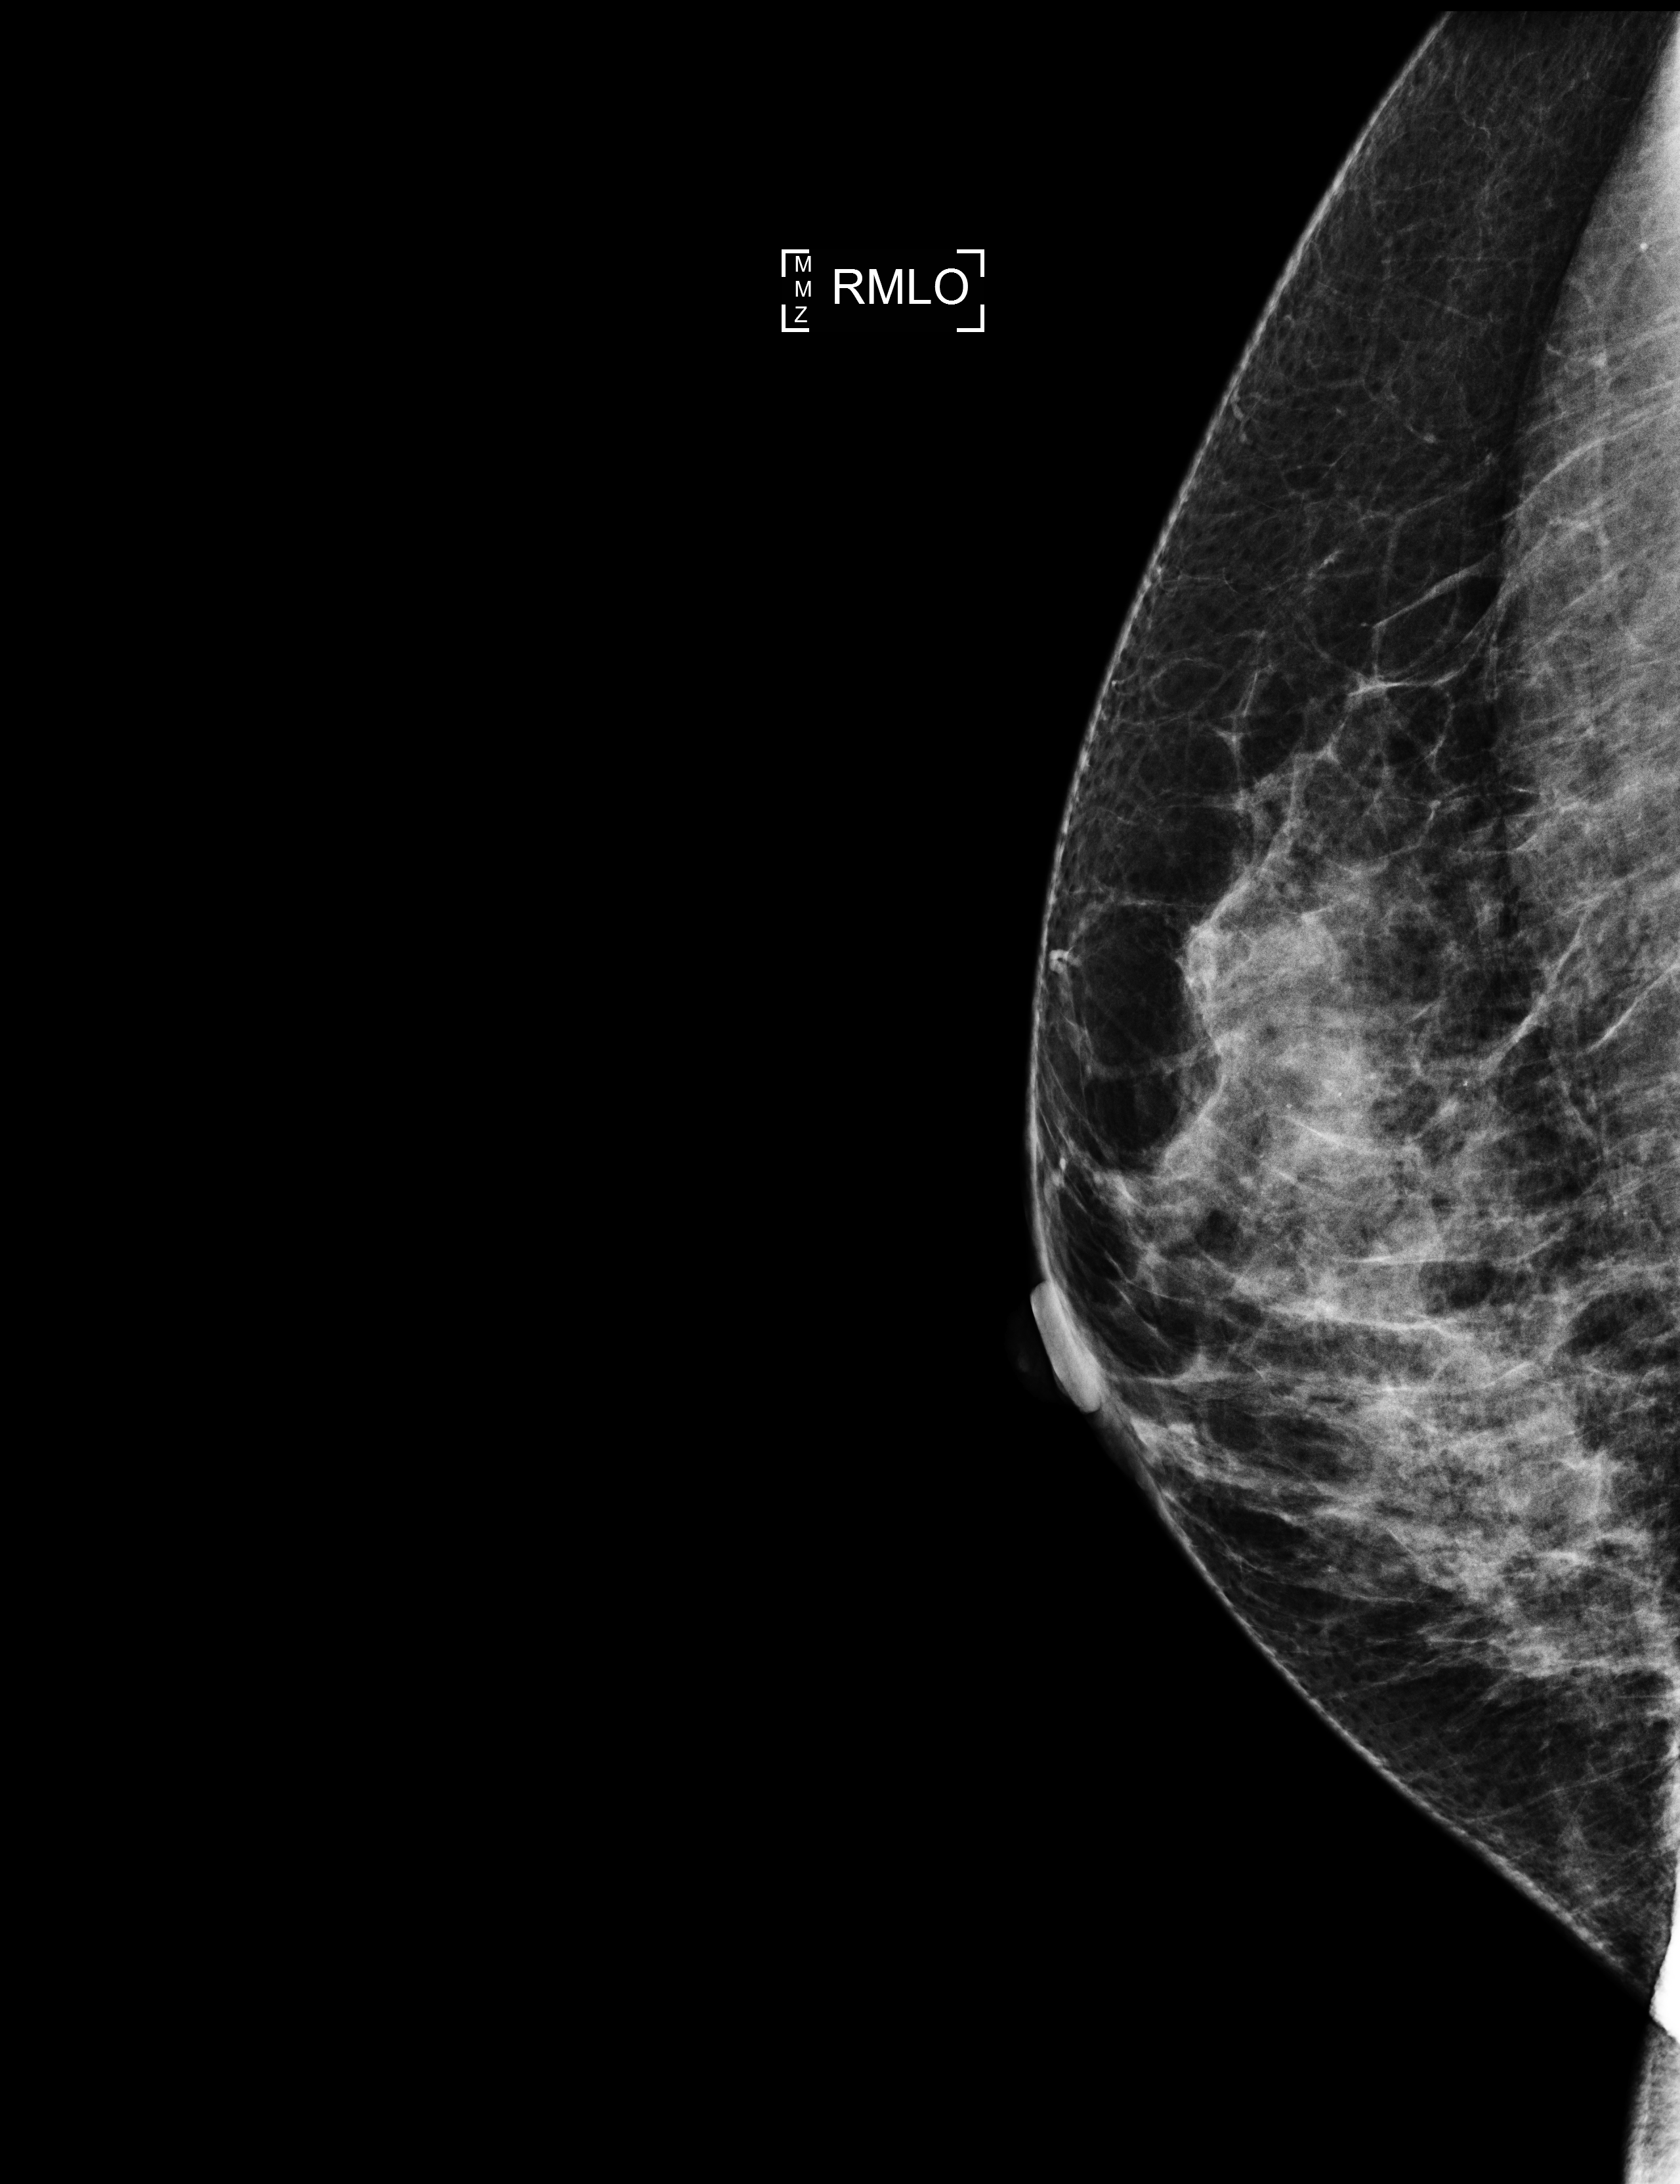
Digital mammogram (FFDM); right breast; medio-lateral oblique projection; screening examination; system: Selenia Dimensions. Female patient, age 47 years.
Breast density at the screening exam (both breasts): heterogeneously dense (BI-RADS density category c). Final BI-RADS category for the screening round (tomosynthesis exam, both breasts): category 1. Recall: no recall after this screen.